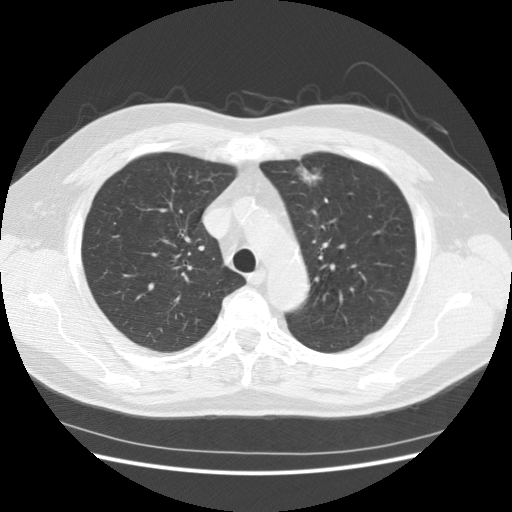
Chest CT (low-dose screening protocol), one axial image; first (baseline) screen; lung window (W 1500 / L -600 HU); slice 42 of 151 in the series; 512 × 512 image matrix. Male, age 63 years at enrolment. Former smoker at enrolment.
• Expert reader's lesion annotation, bounding box <282,155,337,205> (left, top, right, bottom; pixels).
• The exam's reader record, not a measurement of the box and not confirmed to be the same lesion: non-calcified nodule or mass ≥4 mm, lingula, 18 × 9 mm, poorly defined margins, soft tissue attenuation.
• Official screen result: positive, change unspecified: nodule(s) >= 4 mm or enlarging nodule(s), mass(es), or other non-specific abnormalities suspicious for lung cancer.